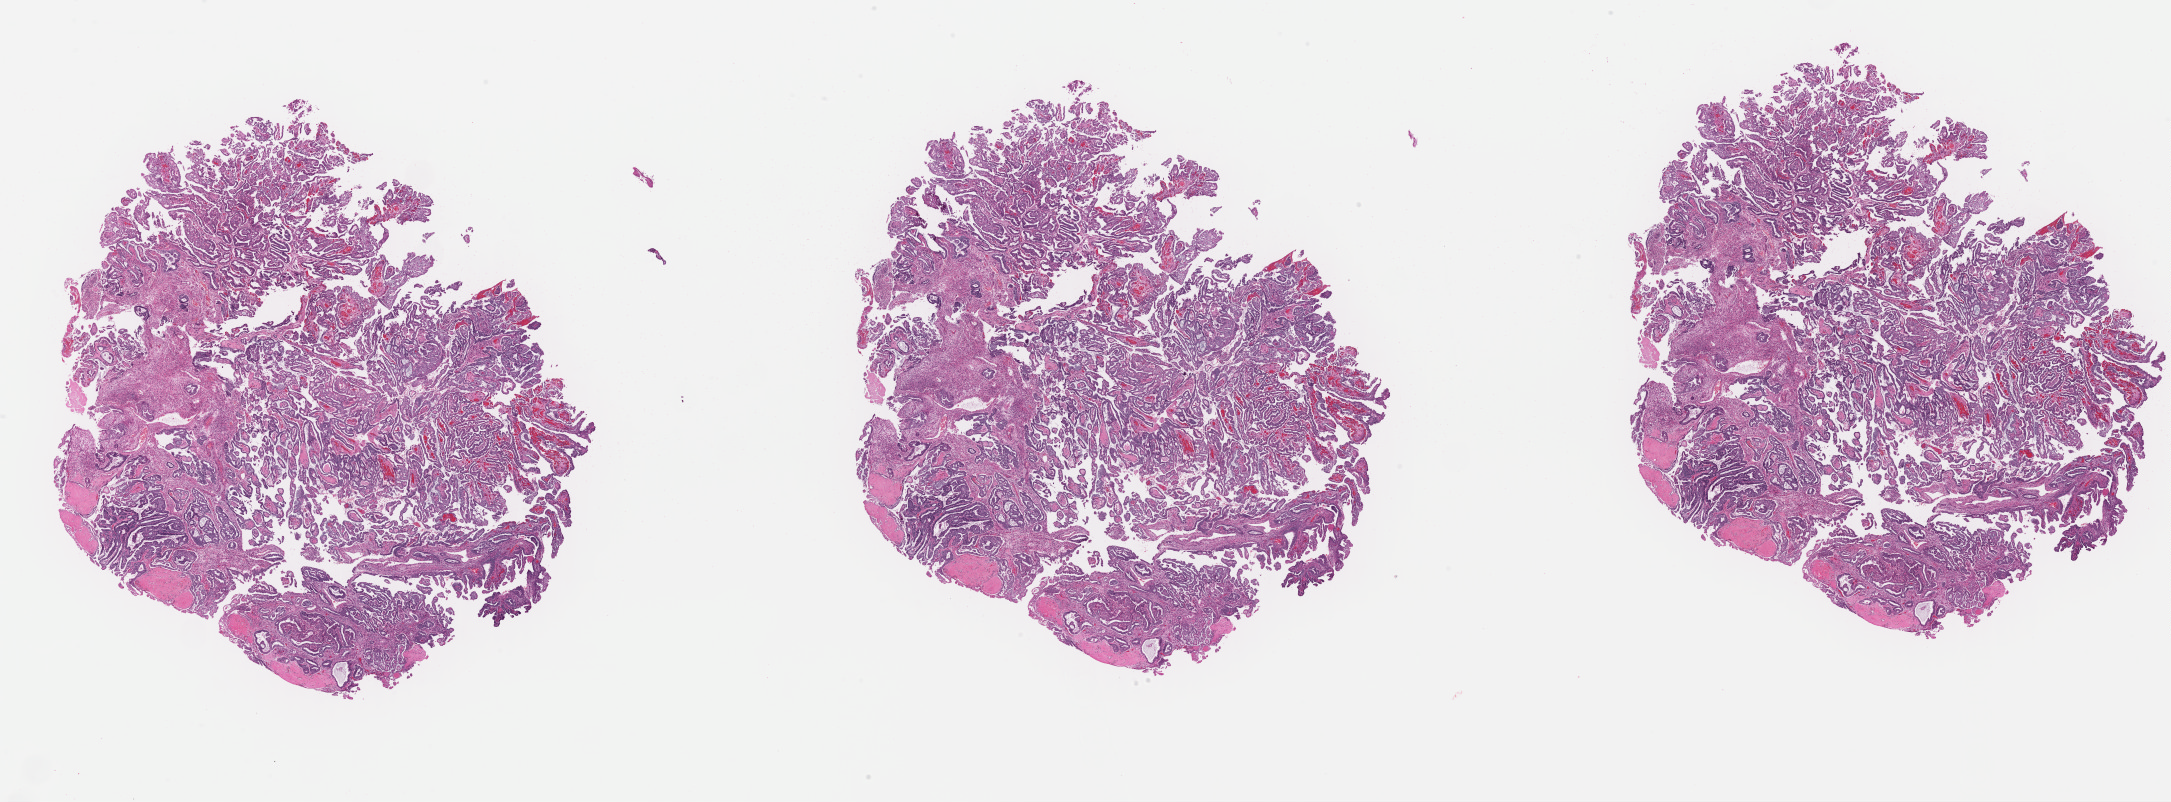
Hematoxylin and eosin (H&E) stained whole-slide image, whole scanned area (about 34.3 x 12.7 mm) shown as a low-resolution overview; formalin-fixed paraffin-embedded (FFPE) diagnostic section; sample: primary tumour, uterus. Patient: female, age at initial diagnosis 68 years. Histologic grade: G1 (well differentiated).
FIGO stage: IIIA. Diagnosis: Endometrioid adenocarcinoma, NOS.